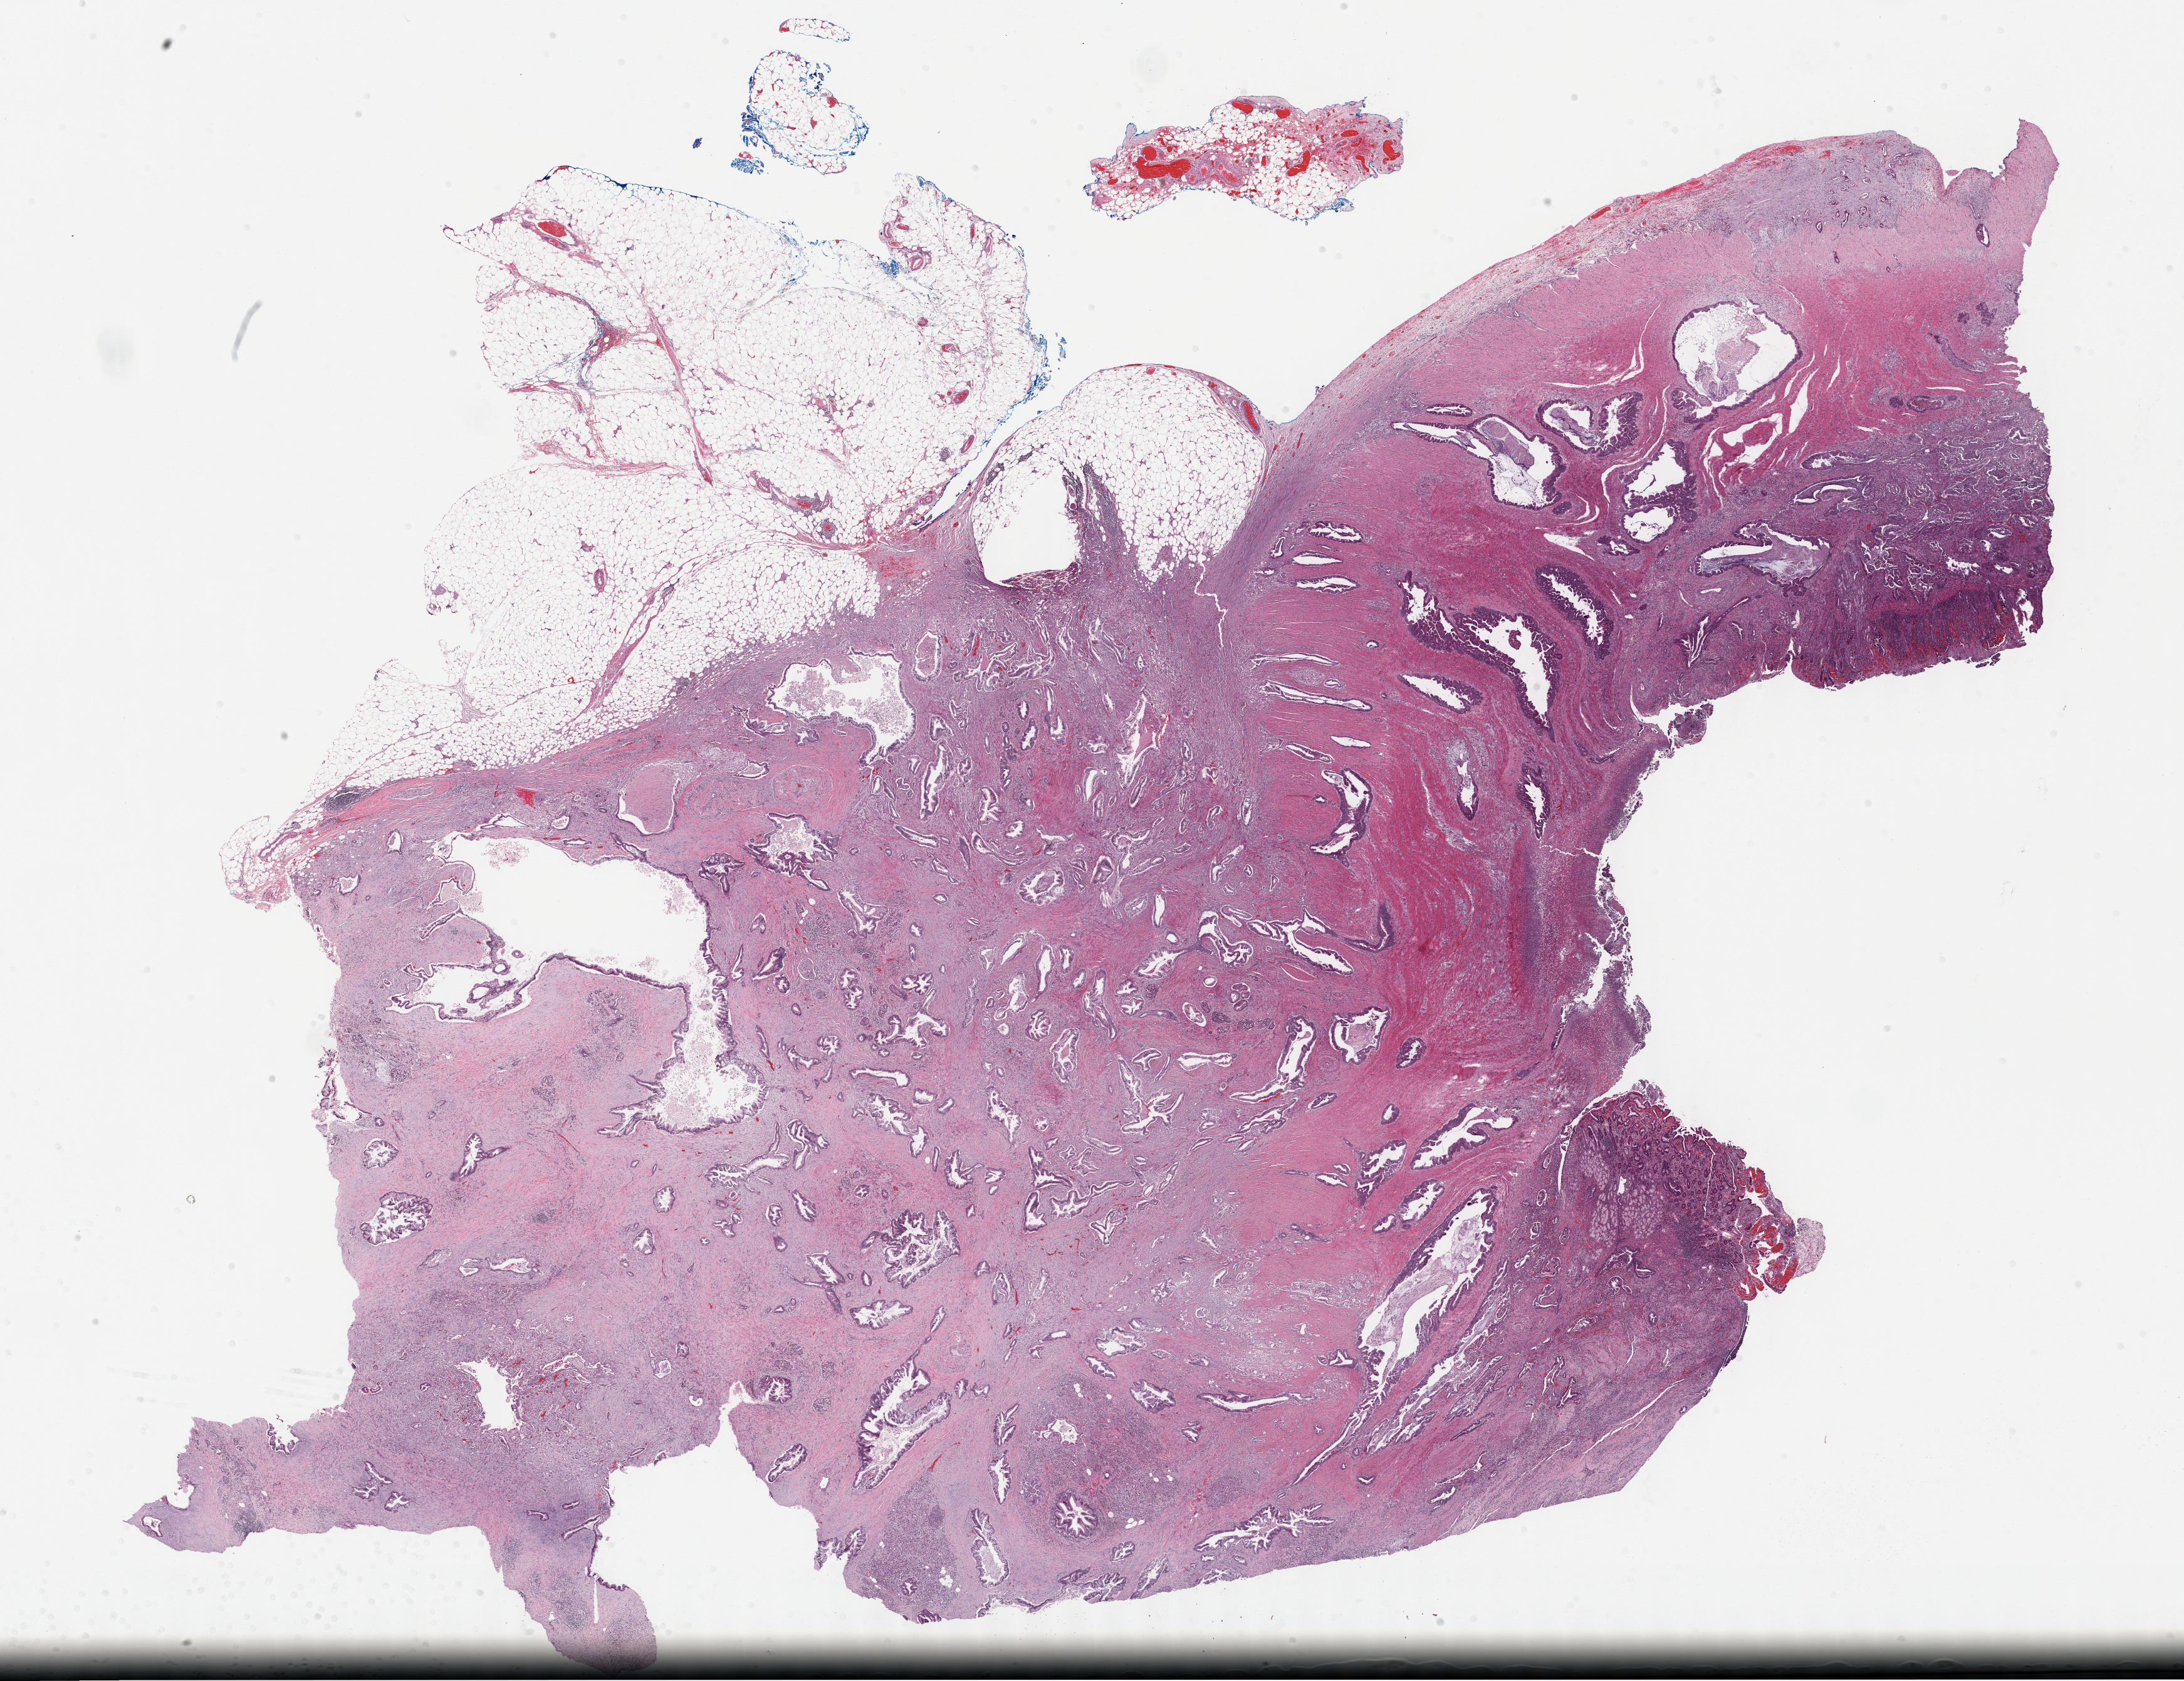
H&E whole-slide image, shown as a low-resolution overview of the whole scanned area (about 28.2 x 21.7 mm); FFPE section; primary tumour sample from the pancreas. Male, age 59 years at initial diagnosis. Histologic grade: G2 (moderately differentiated).
AJCC pathologic stage: IIB. Lymph nodes positive (case pathology): 4 of 17 examined. Pathologic diagnosis: Infiltrating duct carcinoma, NOS (body of pancreas).